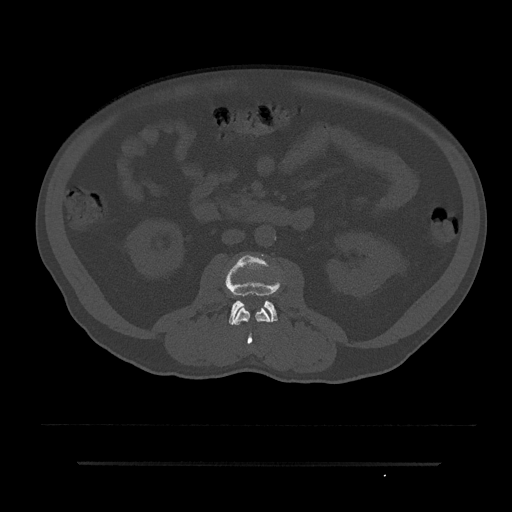
CT including the spine, one axial slice; position 35 of 797 along the scan axis; reconstruction kernel Br40s/3; 120 kVp; bone window (W 1800 / L 400 HU); 512 × 512 image matrix, field of view 464 × 464 mm. Male patient, age 59 years. From the clinical record (not read from this slice): primary cancer: bile ducts.
Annotated regions visible in this slice (semi-automatically segmented with operator editing):
- L2 vertebra: box from (x=233, y=305) to (x=272, y=345) px
- L3 vertebra: (x=226, y=255)–(x=279, y=325)